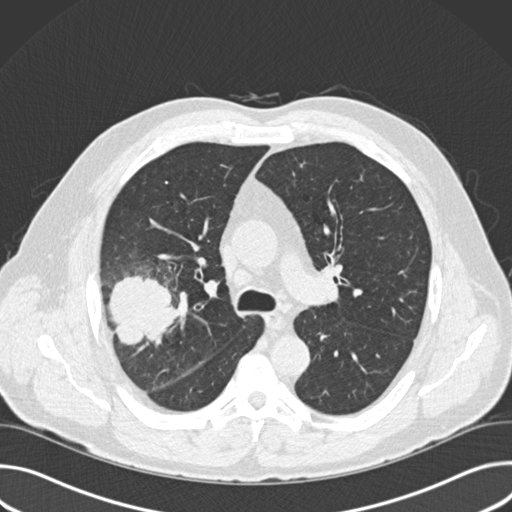
Low-dose screening chest CT, one axial slice; reconstruction kernel B30f; lung window (W 1500 / L -600 HU); 2 mm slice thickness; 512 × 512 image matrix.
Structures marked on this image (expert manual segmentation):
- lesion 1 (tumor, upper lobe of right lung): bounding box (x1, y1, x2, y2) in pixels: (109, 275, 179, 345)